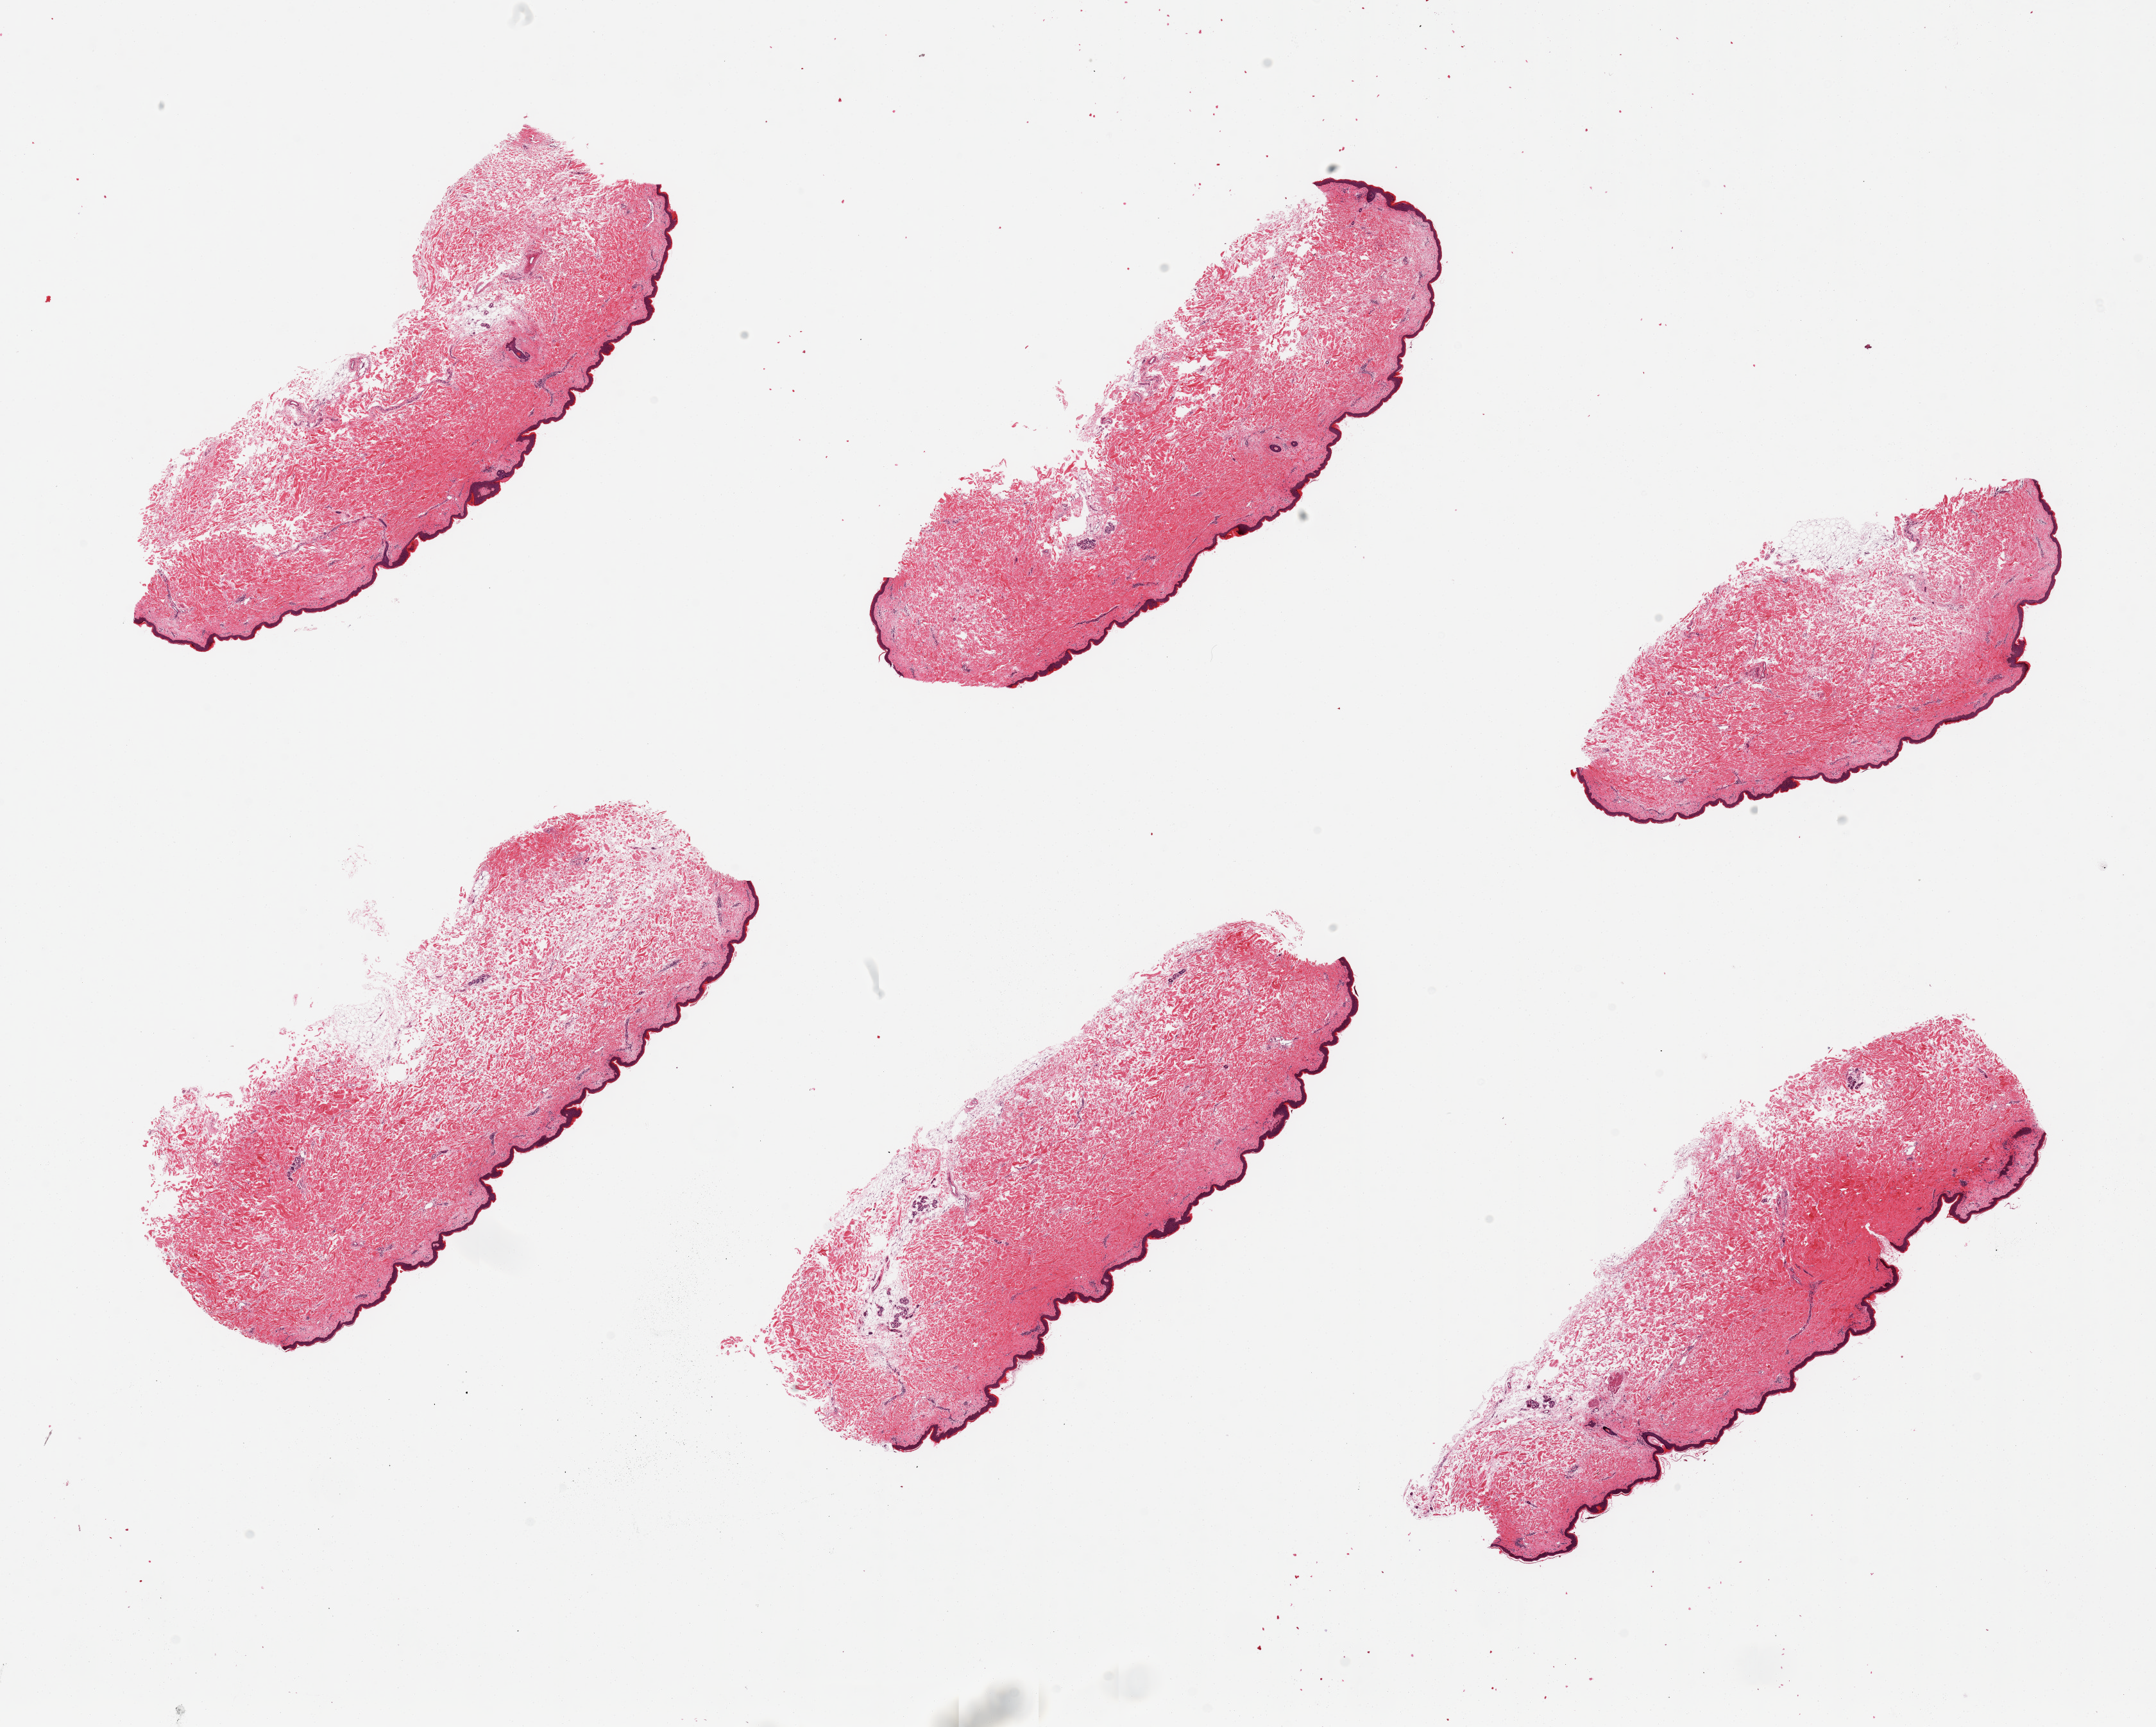
H&E whole-slide image — a low-resolution overview of the entire scanned area, about 26.6 x 21.3 mm (from a 20x scan). PAXgene-fixed paraffin-embedded (PFPE) section. Sampled site (target tissue): skin of suprapubic region. Tissue donor sample. Donor: female.
Reviewer comment on this tissue sample: 6 pieces. Trace dermal fat; Squamous epithelium is ~75 mcirons.